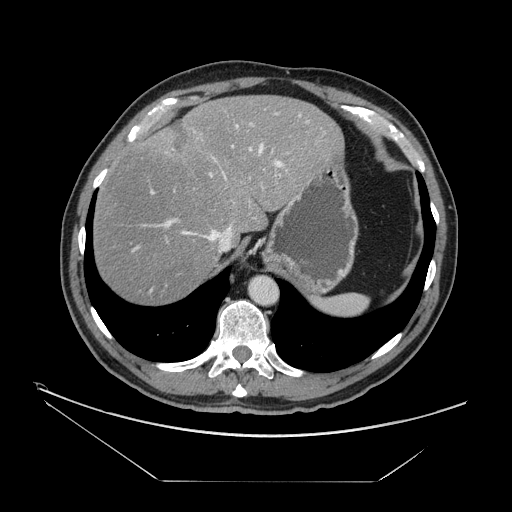
Contrast-enhanced abdominal CT, one axial slice; reconstruction kernel STANDARD; intravenous contrast given; soft-tissue window (W 400 / L 40 HU); 2.5 mm slice thickness; 512 × 512 image matrix. Male patient, age 65 years. Case-level facts recorded for this patient, not image findings: diagnosis: colorectal cancer liver metastases, imaged before liver resection.
Annotated regions visible in this slice (outlined manually by an expert reader):
- hepatic veins: bounding box (x1, y1, x2, y2) in pixels: (182, 145, 263, 253)
- liver: (93, 95, 341, 307)
- planned liver remnant (the part of the liver to remain after resection): (93, 95, 342, 307)
- portal vein (with intrahepatic branches): (150, 112, 308, 228)
- liver metastasis: (174, 124, 189, 153)